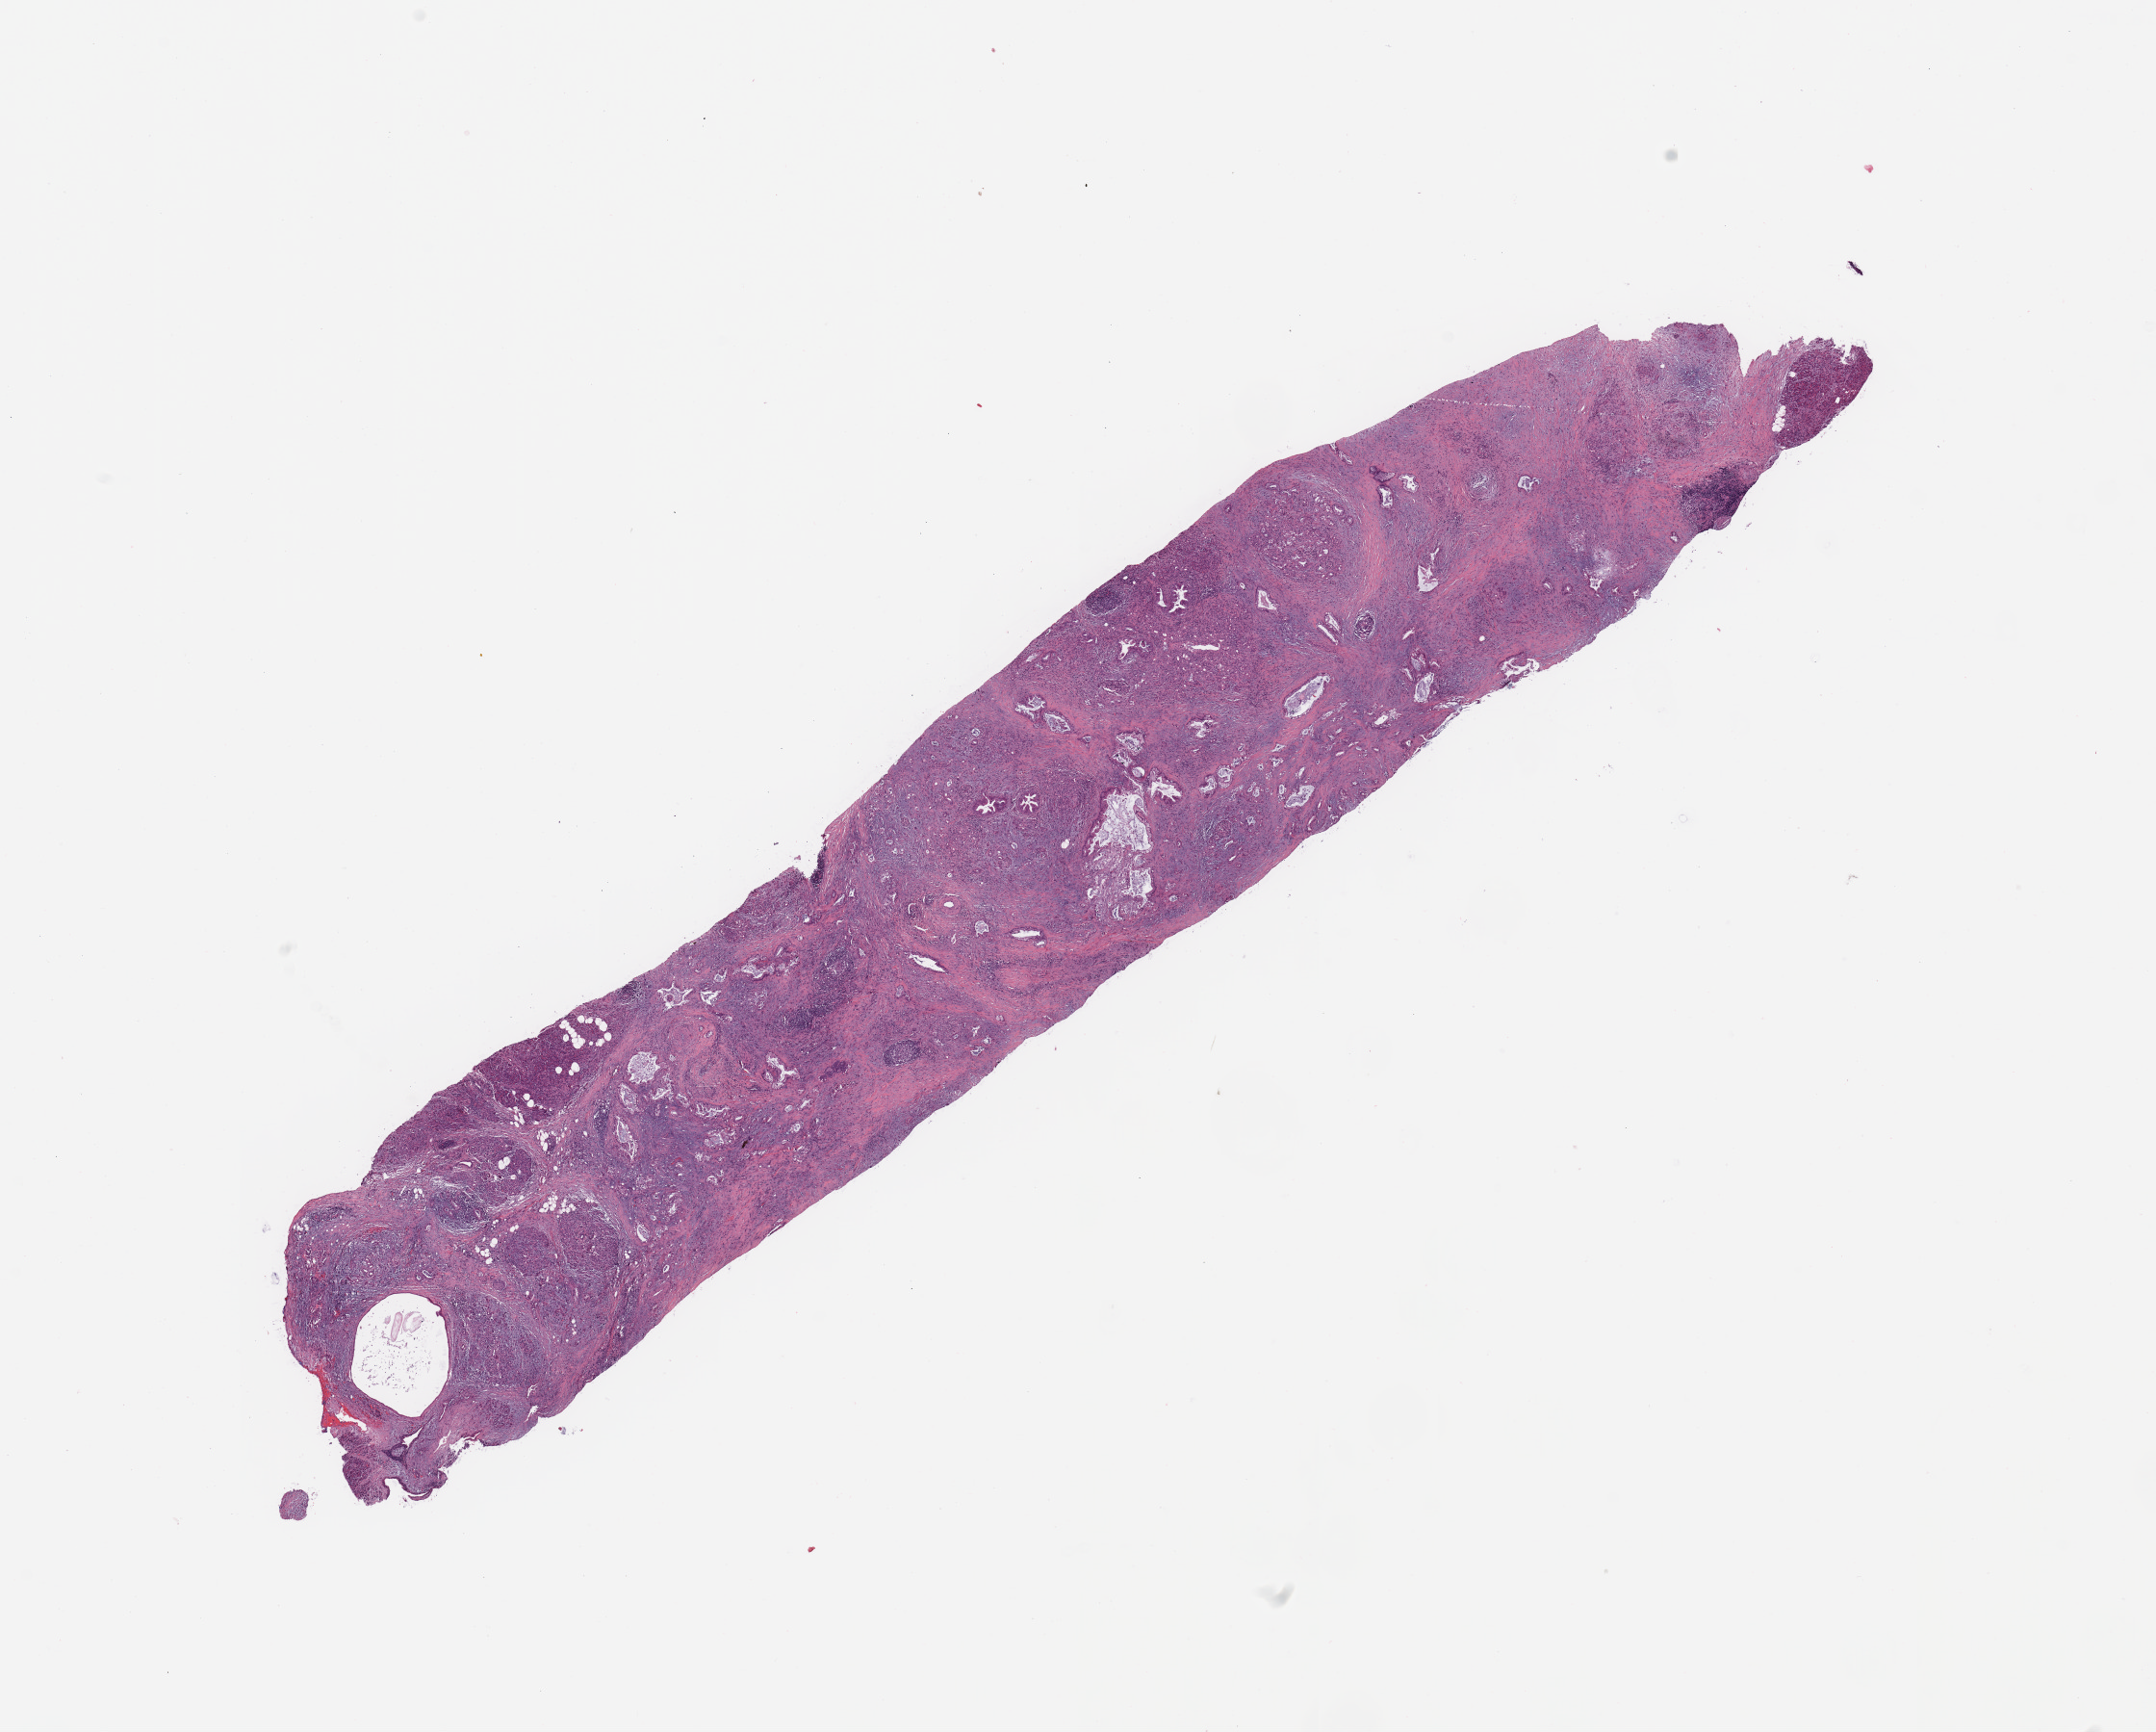
Whole-slide histology image, Hematoxylin and eosin (H&E) stained, whole scanned area (about 17.7 x 14.2 mm) shown as a low-resolution overview, tumour tissue sample, pancreas. 80-year-old male patient. Histologic grade: G2 (moderately differentiated).
• AJCC pathologic stage: IIB
• histologic diagnosis: Infiltrating duct carcinoma, NOS
• primary tumour site (as recorded): head